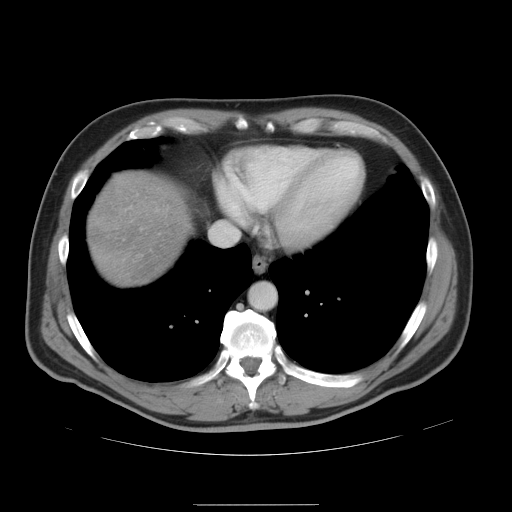
Contrast-enhanced abdominal CT, one axial slice. Slice 44 of 47 in the series (ordered by position). Soft-tissue window (W 400 / L 40 HU). 512 × 512 image matrix. Male patient, age 61 years. Case-level facts recorded for this patient, not image findings: diagnosis: colorectal cancer liver metastases, imaged before liver resection; multiple liver metastases: no; largest metastasis: 1.2 cm; disease in both lobes: no.
Outlined on this slice (manually delineated by an expert):
- liver: bounding box [x1, y1, x2, y2] px = [88, 170, 194, 288]
- planned liver remnant (the part of the liver to remain after resection): [88, 170, 194, 288]